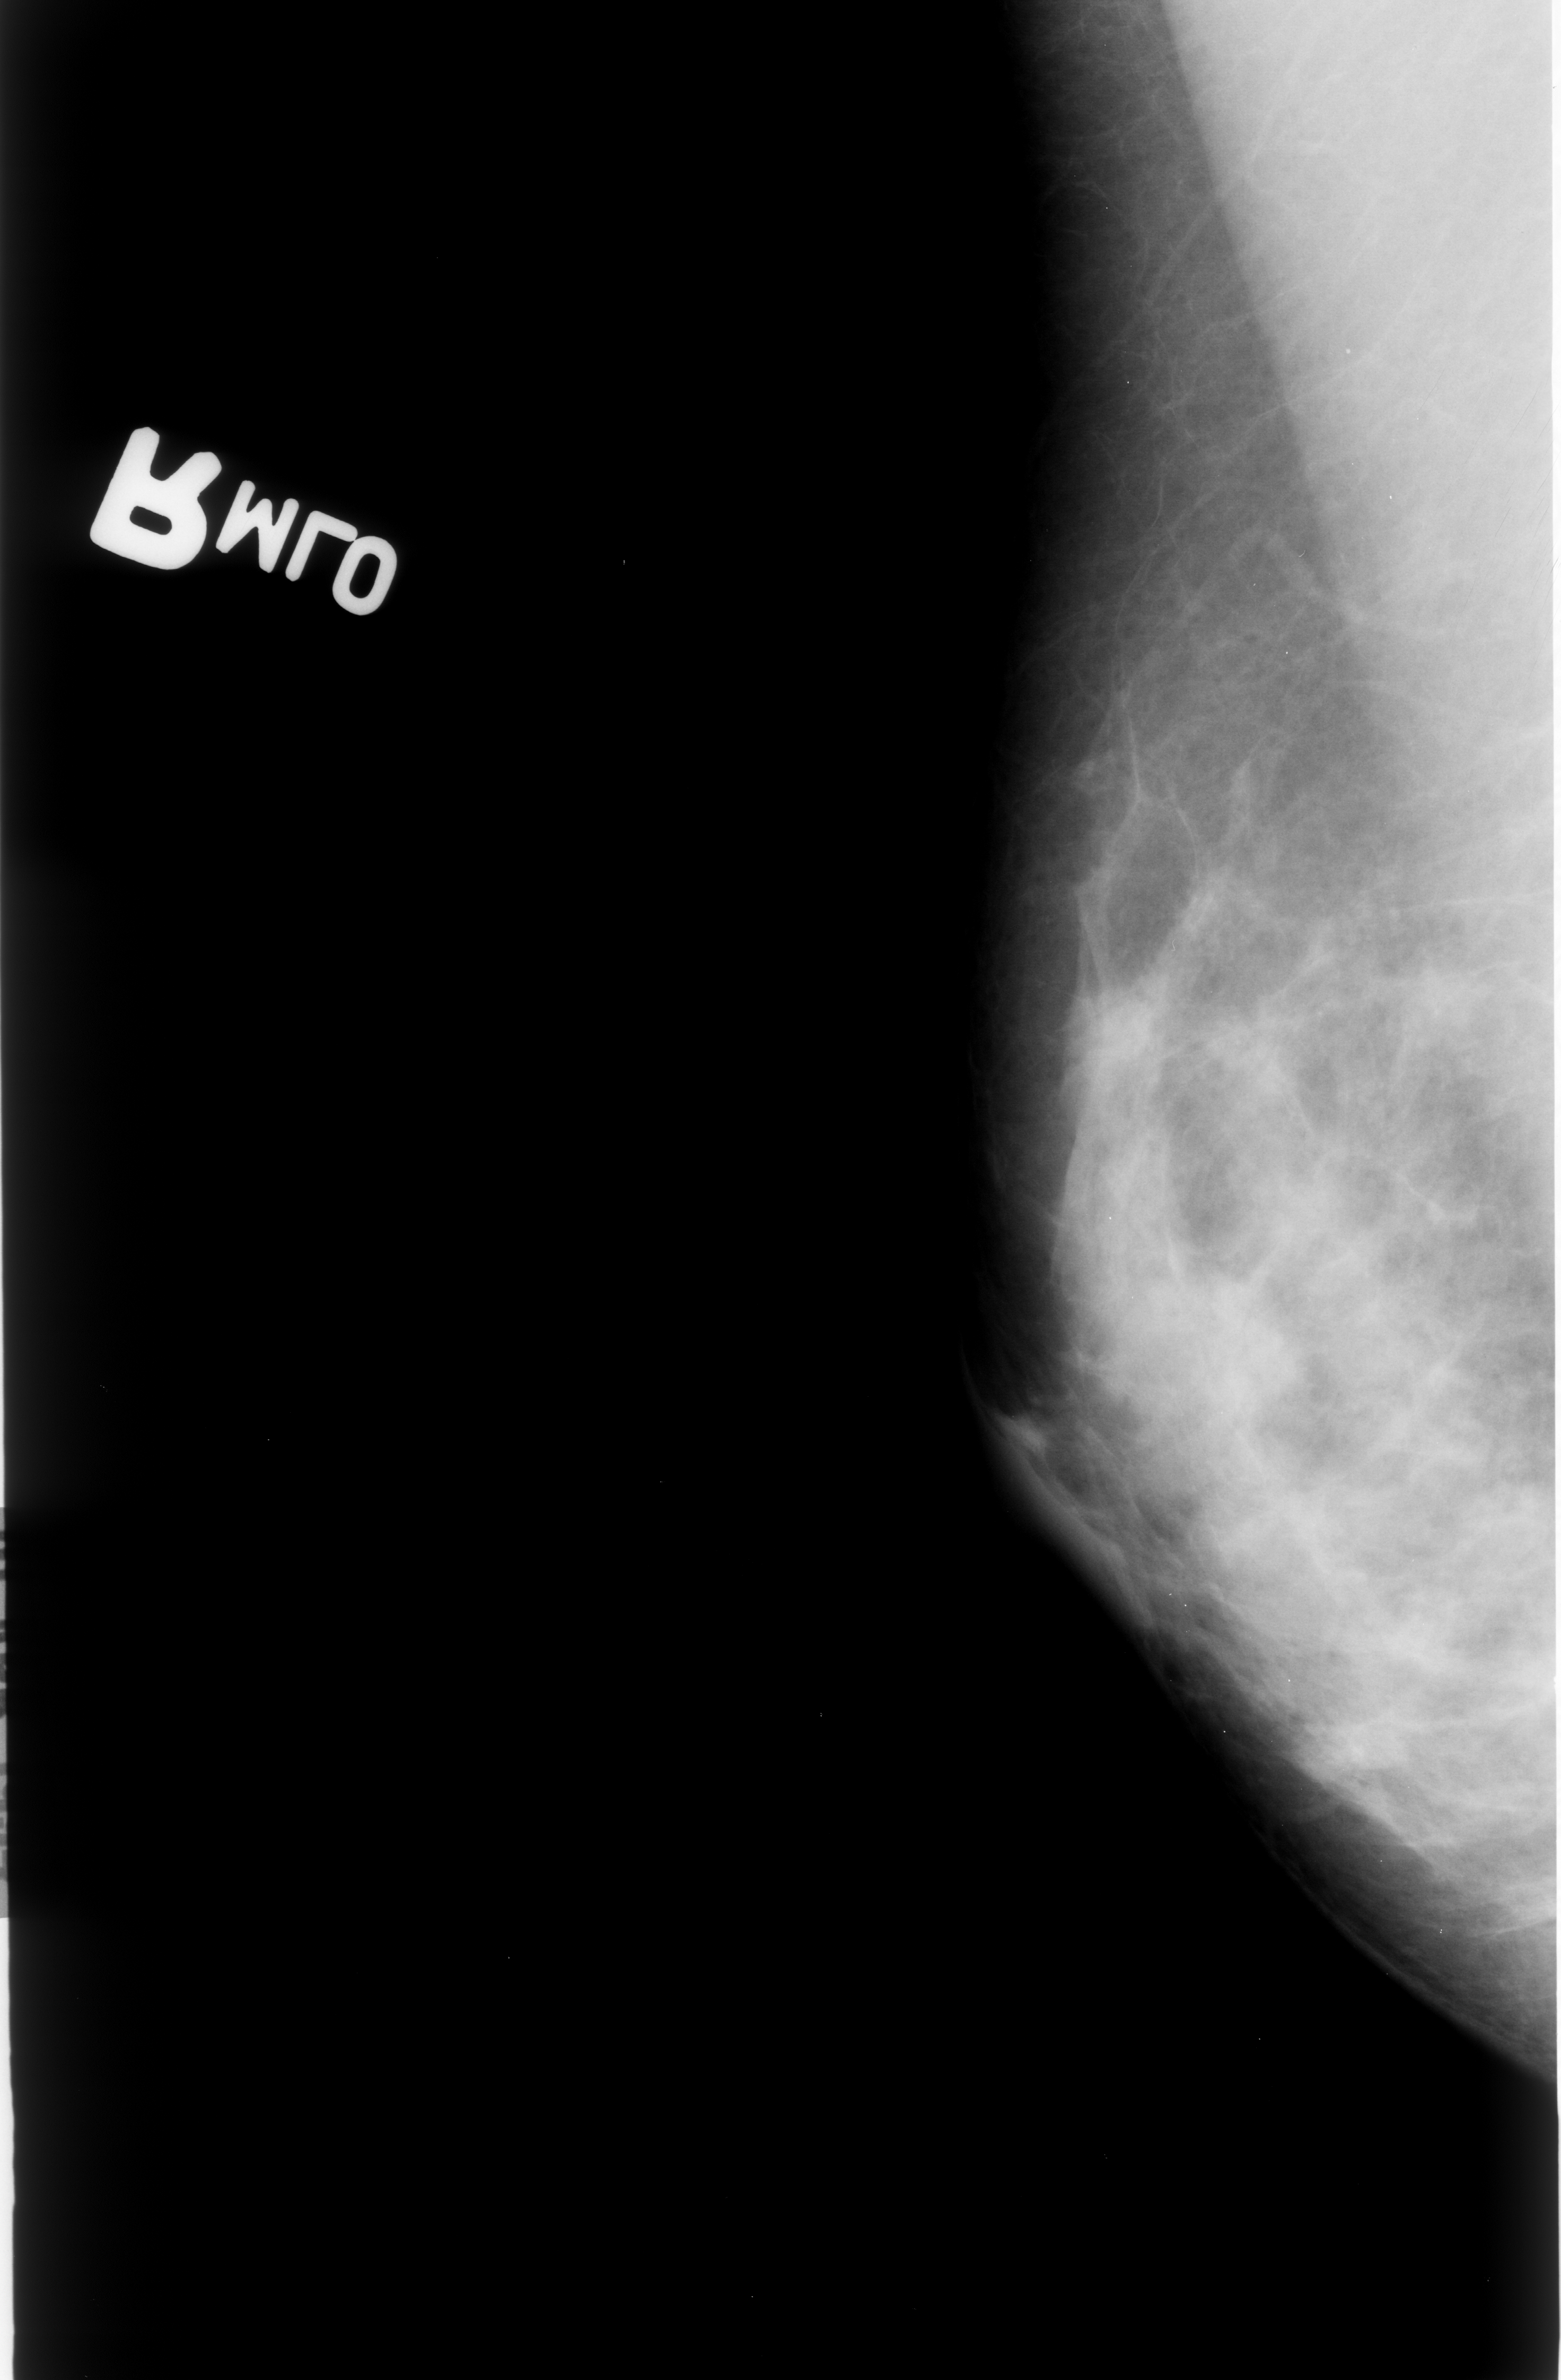
Mammogram (digitized film); right breast; MLO view; BI-RADS breast density category 3 (scale 1–4).
Abnormality record for this image: mass, shape irregular, margins obscured / ill defined; BI-RADS assessment category 3; subtlety rating 1 on a 1 (subtle) to 5 (obvious) scale; pathology result (as recorded, not read from the image): malignant.